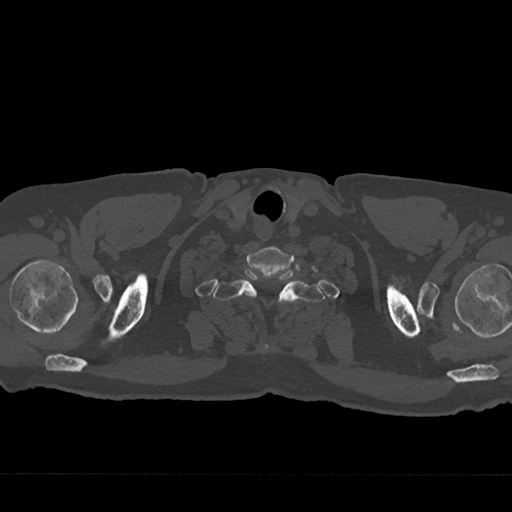
CT including the spine, one axial slice; reconstruction kernel Br40s/3; bone window (W 1800 / L 400 HU); 512 × 512 image matrix, field of view 377 × 377 mm. Male patient, age 75 years. Case-level facts recorded for this patient, not image findings: primary cancer: renal; vertebrae with lytic lesions (as recorded): T4.
Structures marked on this image (semi-automatic segmentation, software-assisted and operator-edited):
- T1 vertebra: bounding box <213,269,324,349> (left, top, right, bottom; pixels)